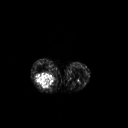
FDG PET of an extremity soft-tissue mass (from a PET/CT study), one axial slice. Position 179 of 267 along the scan axis. 3.27 mm slice thickness. 128 × 128 image matrix, field of view 500 × 500 mm. Female patient, age 62 years. Case-level facts recorded for this patient, not image findings: histological type: liposarcoma; site of the primary tumour: right thigh.
Structures marked on this image (expert contour drawn on MRI and transferred to this co-registered scan by the dataset authors):
- gross tumour volume (mass): box from (x=35, y=72) to (x=55, y=89) px